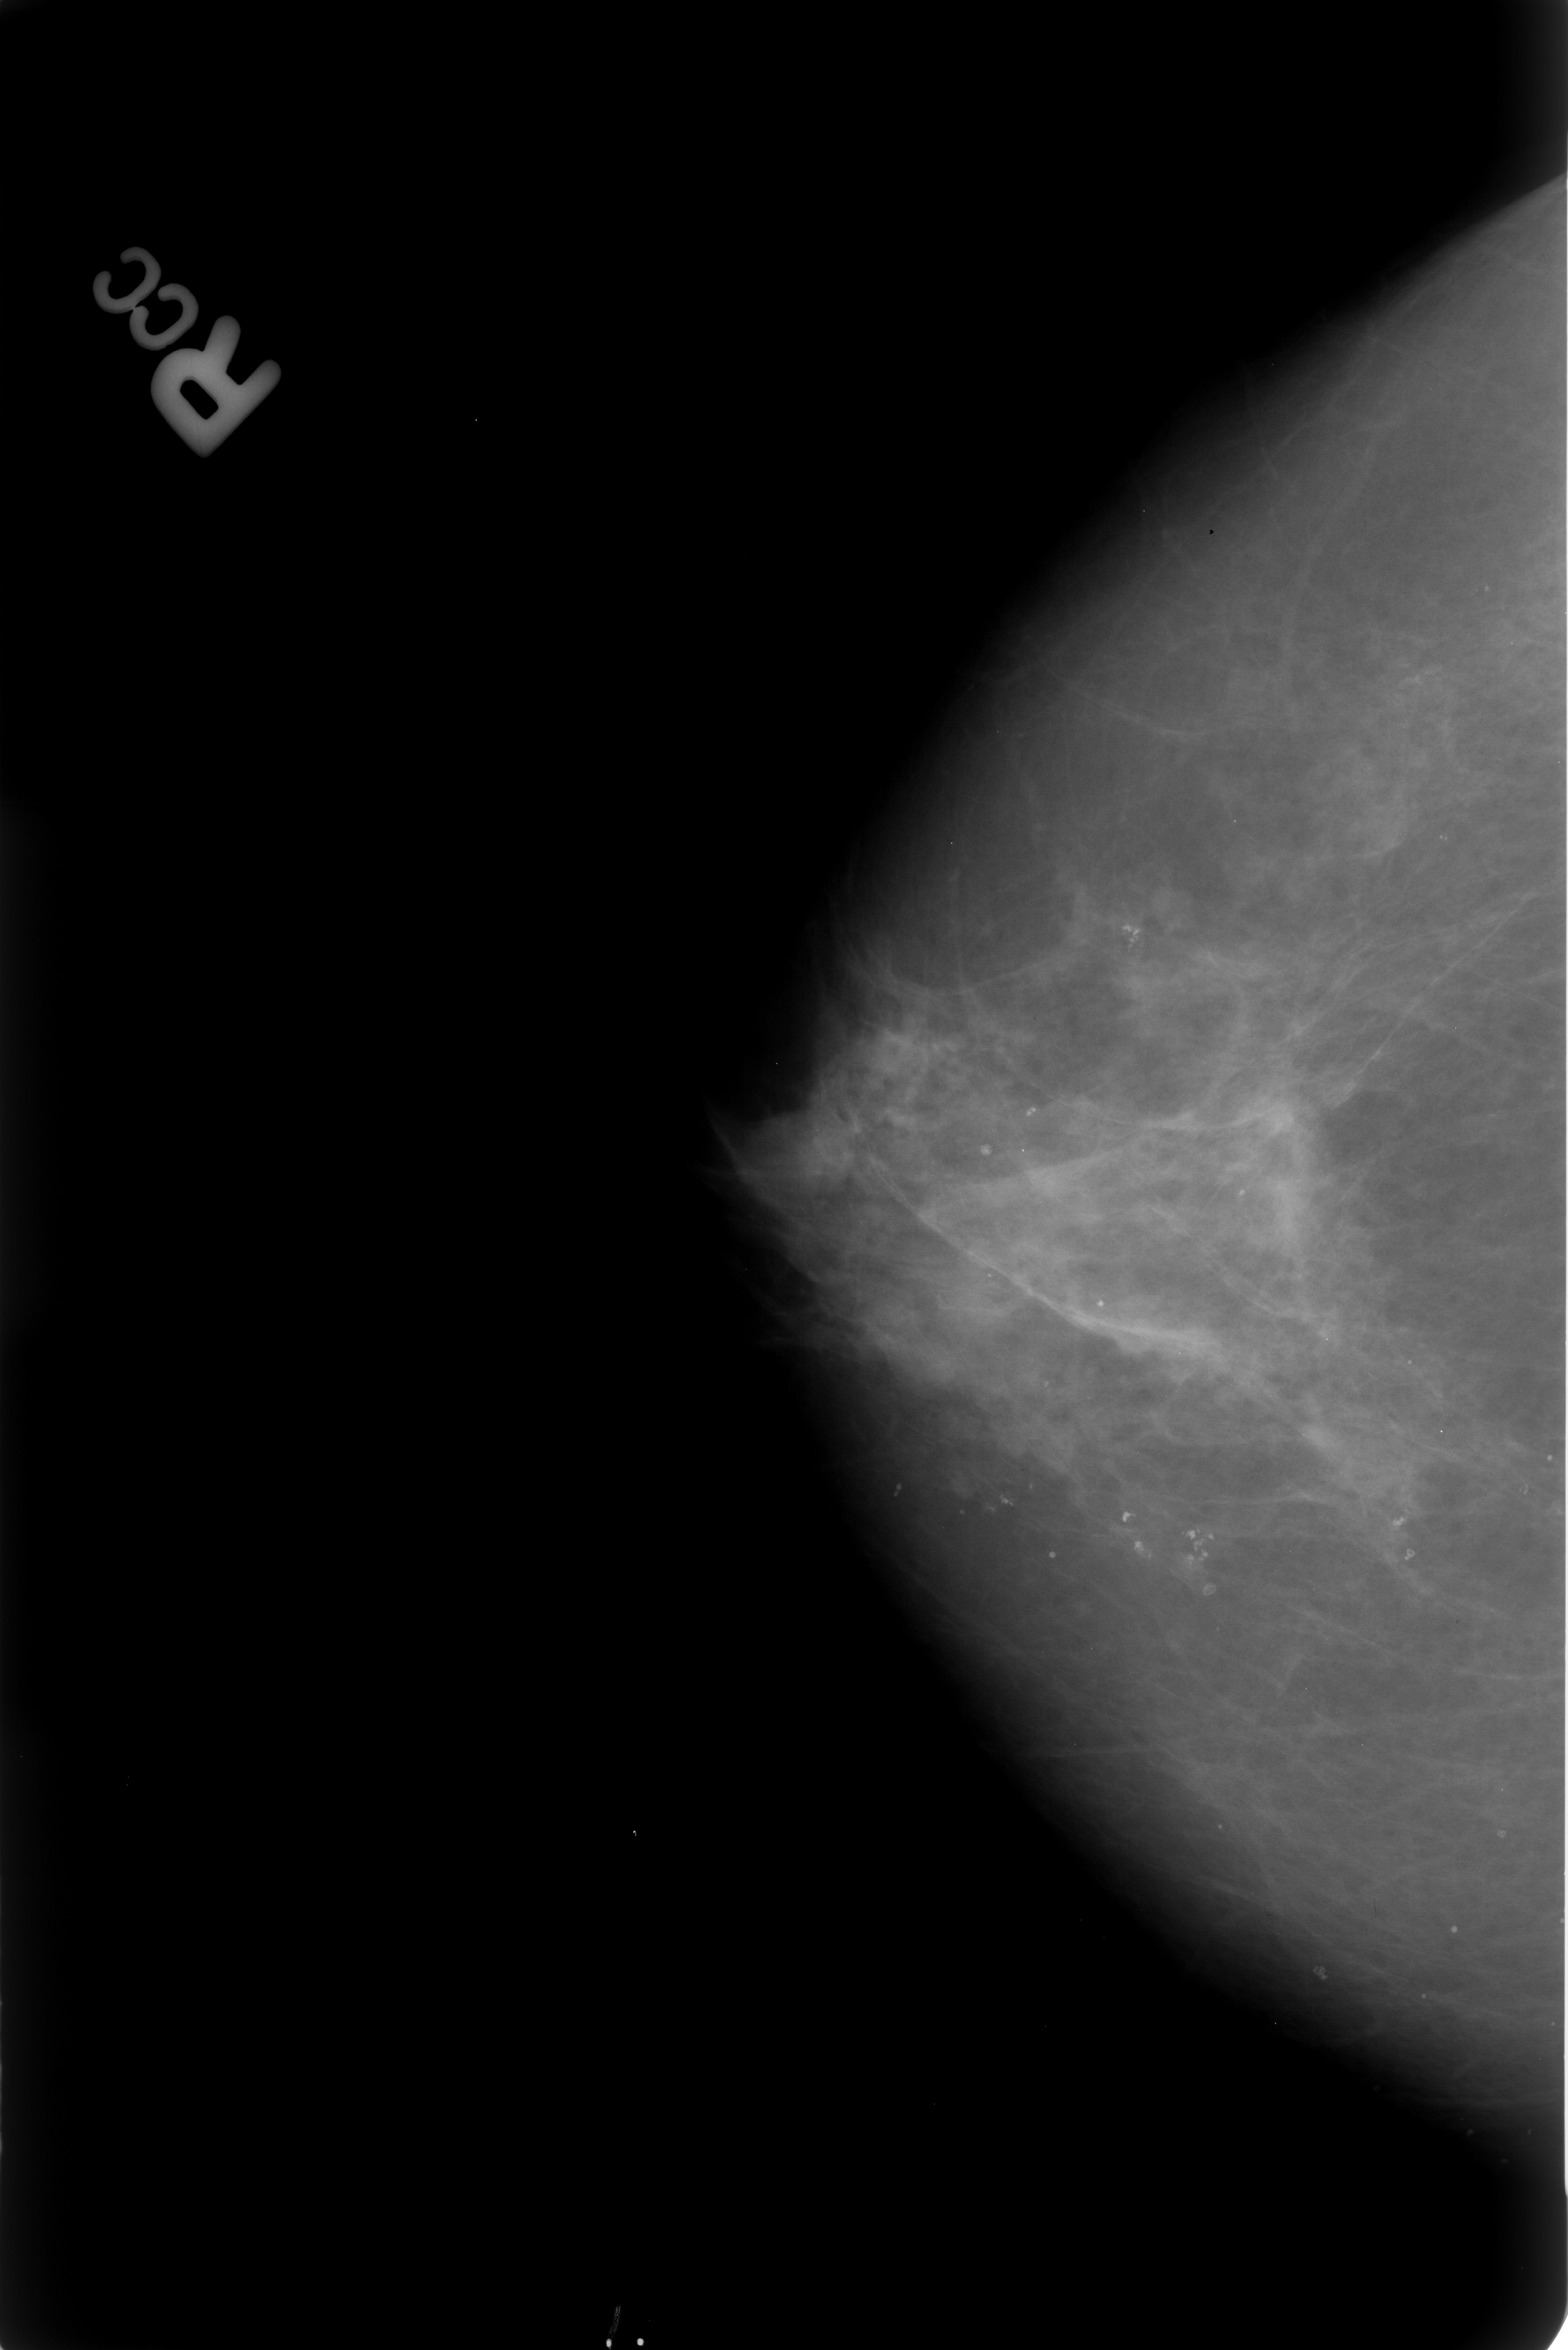
Scanned film-screen mammogram; right breast; craniocaudal (CC) view; BI-RADS breast density category 2 (scale 1–4).
- Radiologist-marked abnormalities on this image: Finding 1 of 4: calcifications, morphology pleomorphic, distribution clustered; BI-RADS assessment category 2; subtlety rating 4 on a 1 (subtle) to 5 (obvious) scale; benign without callback (not worked up further).
- Finding 2 of 4: calcifications, morphology pleomorphic, distribution clustered; BI-RADS assessment category 2; benign; no additional work-up was recommended (benign without callback).
- Finding 3 of 4: calcifications, morphology pleomorphic, distribution clustered; BI-RADS assessment category 2; subtlety rating 4 on a 1 (subtle) to 5 (obvious) scale; benign; no additional work-up was recommended (benign without callback).
- Finding 4 of 4: calcifications, morphology pleomorphic, distribution clustered; BI-RADS assessment category 2; subtlety rating 4 on a 1 (subtle) to 5 (obvious) scale; benign; no additional work-up was recommended (benign without callback).